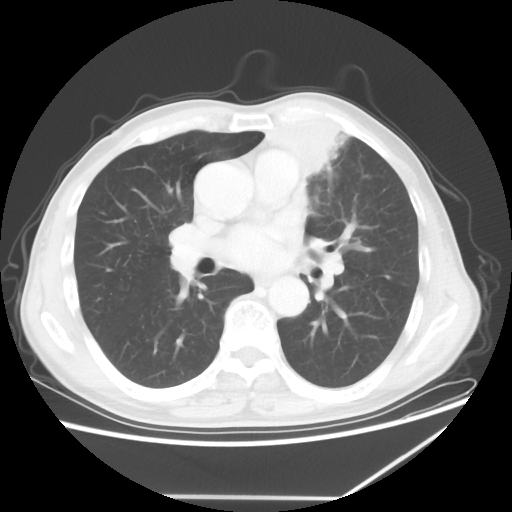
Chest CT, one axial slice; position 33 of 64 along the scan axis; 100 kVp; lung window (W 1500 / L -600 HU); 5 mm slice thickness; 512 × 512 image matrix. Male patient, age 64 years. Case-level facts recorded for this patient, not image findings: clinical TNM (as recorded): T1c N1 M1.
Annotated regions visible in this slice (rectangle marked by the reading radiologist):
- lung tumour (recorded histology: squamous cell carcinoma): box from (x=254, y=100) to (x=383, y=208) px